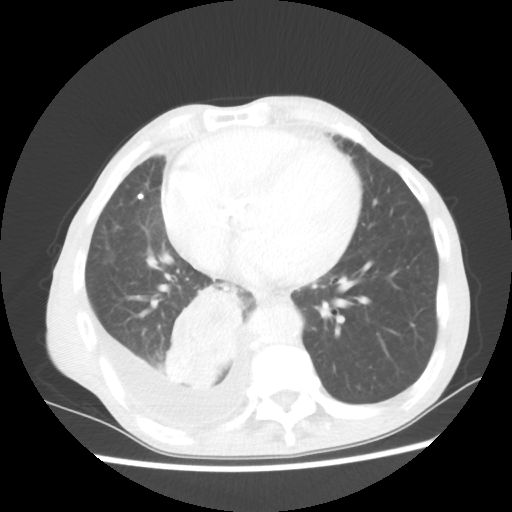
Chest CT, one axial slice; position 23 of 60 along the scan axis; reconstruction kernel STANDARD; 80 kVp; lung window (W 1500 / L -600 HU); 5 mm slice thickness; 512 × 512 image matrix, field of view 335 × 335 mm. Male patient, age 76 years. From the clinical record (not read from this slice): clinical TNM (as recorded): T3 N3 M1a; histopathological grade: G3.
Annotated regions visible in this slice (bounding box drawn by a radiologist):
- lung tumour (recorded histology: squamous cell carcinoma): bounding box (x1, y1, x2, y2) in pixels: (161, 280, 246, 392)